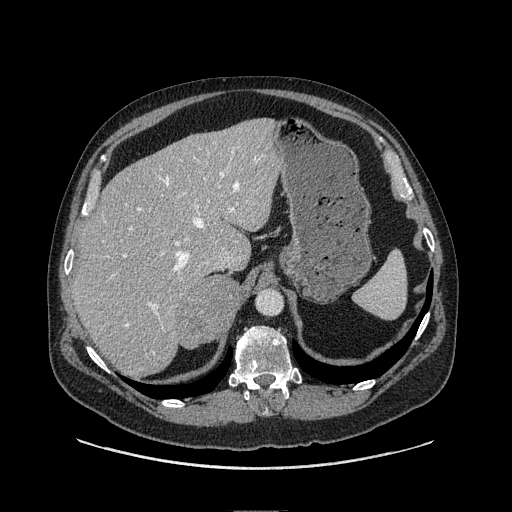
Contrast-enhanced abdominal CT, one axial slice. Position 78 of 149 along the scan axis. Soft-tissue window (W 400 / L 40 HU). 1.25 mm slice thickness. 512 × 512 image matrix, field of view 440 × 440 mm. Male patient. Case-level facts recorded for this patient, not image findings: diagnosis: adrenocortical carcinoma; tumour side: right adrenal; tumour size at pathology: 7.5 cm.
Structures marked on this image (semi-automatic segmentation, software-assisted and operator-edited):
- mass: box from (x=181, y=277) to (x=241, y=346) px